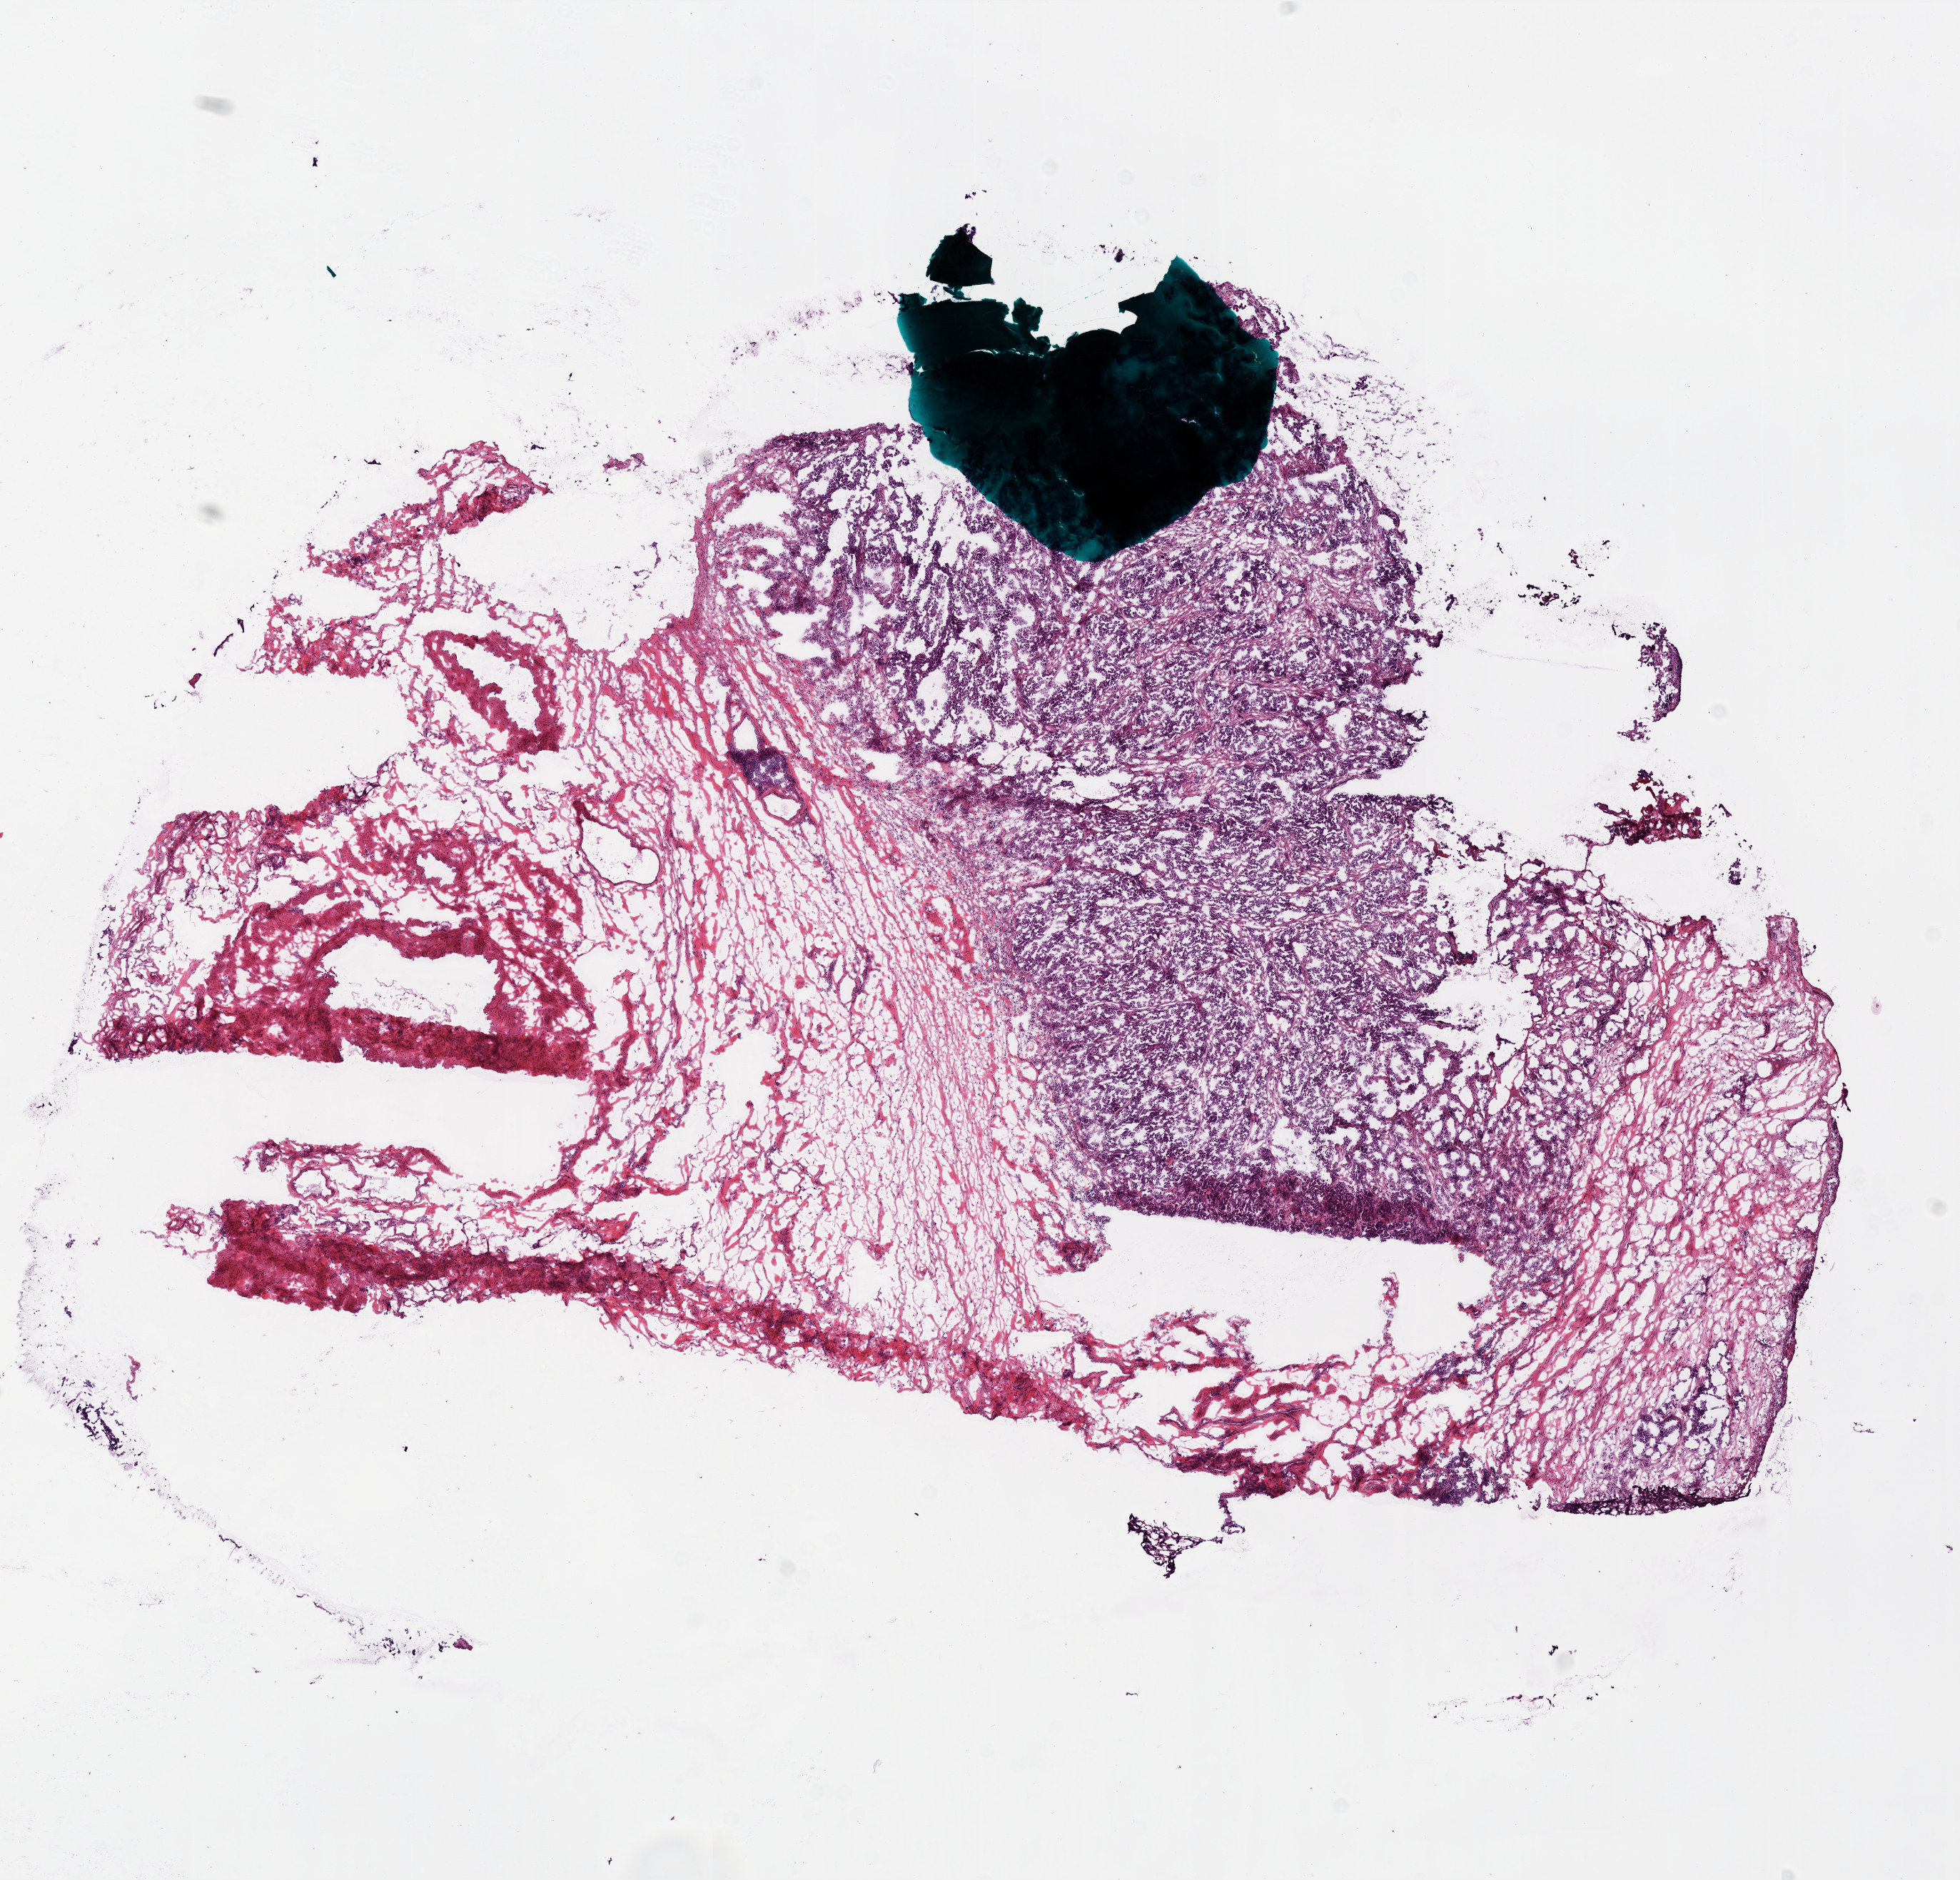
H&E whole-slide image, shown as a low-resolution overview of the whole scanned area (about 11.0 x 10.5 mm). Frozen section from the bottom of the tissue portion. Ovary, primary tumour sample. Female, age 42 years at initial diagnosis. Histologic grade: G3 (poorly differentiated). Slide review estimates, as recorded: tumour nuclei 80%, normal cells 0%, necrosis 5%.
• FIGO stage: IIIC
• histologic diagnosis: Serous cystadenocarcinoma, NOS
• laterality: left